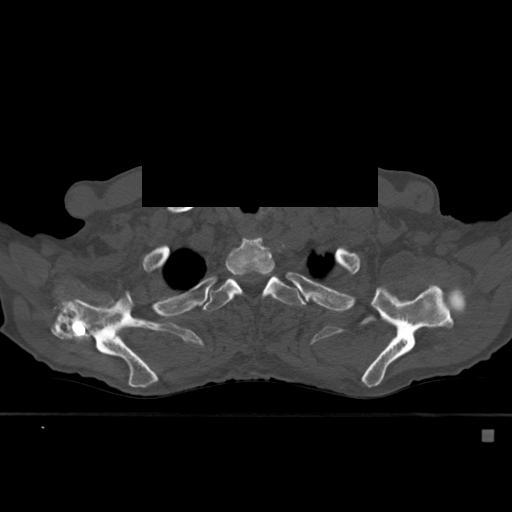
CT including the spine, one axial slice; position 439 of 527 along the scan axis; bone window (W 1800 / L 400 HU); 1.5 mm slice thickness; 512 × 512 image matrix. Male patient, age 78 years. From the clinical record (not read from this slice): primary cancer: prostate.
Structures marked on this image (semi-automatic segmentation, software-assisted and operator-edited):
- T2 vertebra: bounding box [x1, y1, x2, y2] px = [225, 238, 277, 298]
- T3 vertebra: [203, 274, 303, 311]